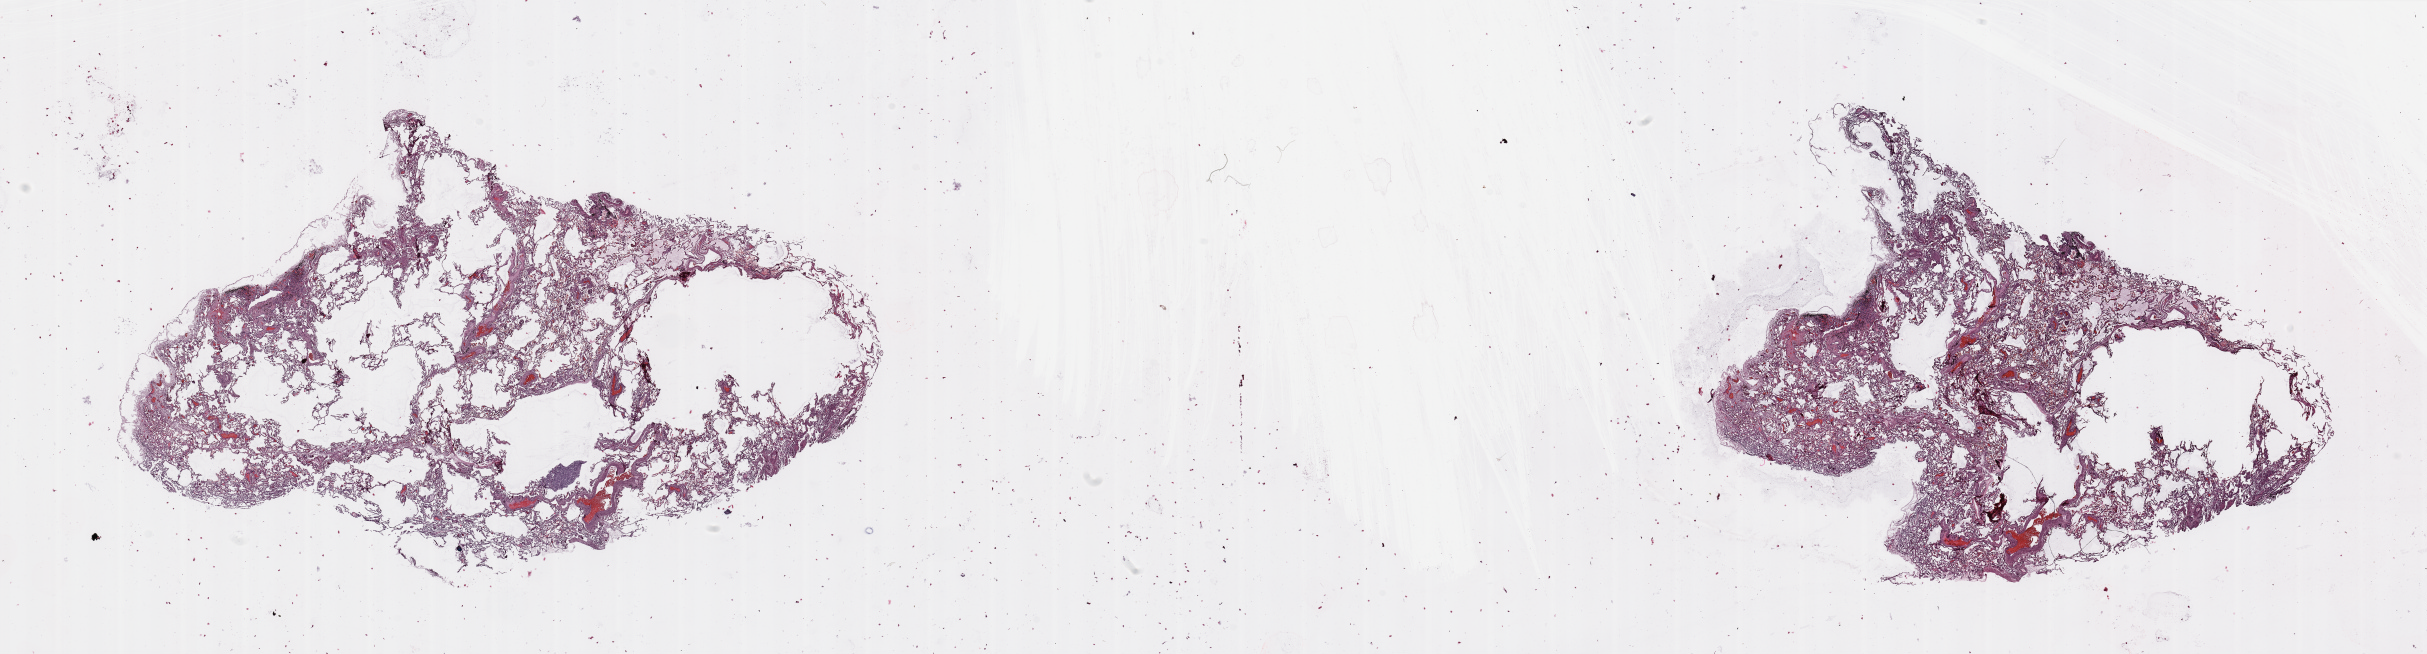
H&E whole-slide image, shown as a low-resolution overview of the whole scanned area (about 38.4 x 10.3 mm, slide scanned at 20x). Normal (non-tumour) tissue sample, lung. 70-year-old male patient.
- this section: normal (non-tumour) tissue from the same patient
- patient diagnosis: Squamous cell carcinoma, NOS